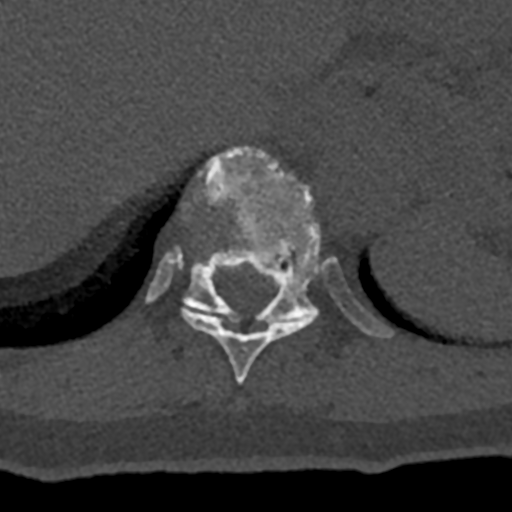
CT including the spine, one axial slice. Position 578 of 797 along the scan axis. Bone window (W 1800 / L 400 HU). 512 × 512 image matrix, field of view 160 × 160 mm. Patient: male, 74 years. From the clinical record (not read from this slice): primary cancer: renal; vertebrae with lytic lesions (as recorded): T10, L1, L2, L3, L4, L5.
Annotated regions visible in this slice (semi-automatic segmentation, software-assisted and operator-edited):
- T10 vertebra: box from (x=181, y=304) to (x=313, y=385) px
- T11 vertebra: (x=145, y=147)–(x=393, y=338)